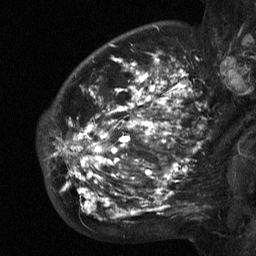
Breast MRI (dynamic contrast-enhanced), one sagittal slice. Position 43 of 64 along the scan axis. Dynamic contrast-enhanced study with each time point stored as its own series, time point 2 of 3 at this slice position (early post-contrast, ordered by acquisition time). 1.5 T. TE 4.8 ms, TR 27 ms. 2.3 mm slice thickness. 256 × 256 image matrix, field of view 200 × 200 mm. Female patient, age 50 years. Case-level facts recorded for this patient, not image findings: setting: breast cancer imaged before/during neoadjuvant chemotherapy; receptor status: HER2-positive.
Structures marked on this image (semi-automatic segmentation, software-assisted and operator-edited):
- analysis volume of interest (the breast-tissue region the enhancement analysis was run in; not a lesion): bounding box [x1, y1, x2, y2] px = [53, 64, 211, 218]
- tumour enhancement mask (voxels above the 90 % enhancement threshold inside the analysis volume of interest): [53, 64, 201, 218]